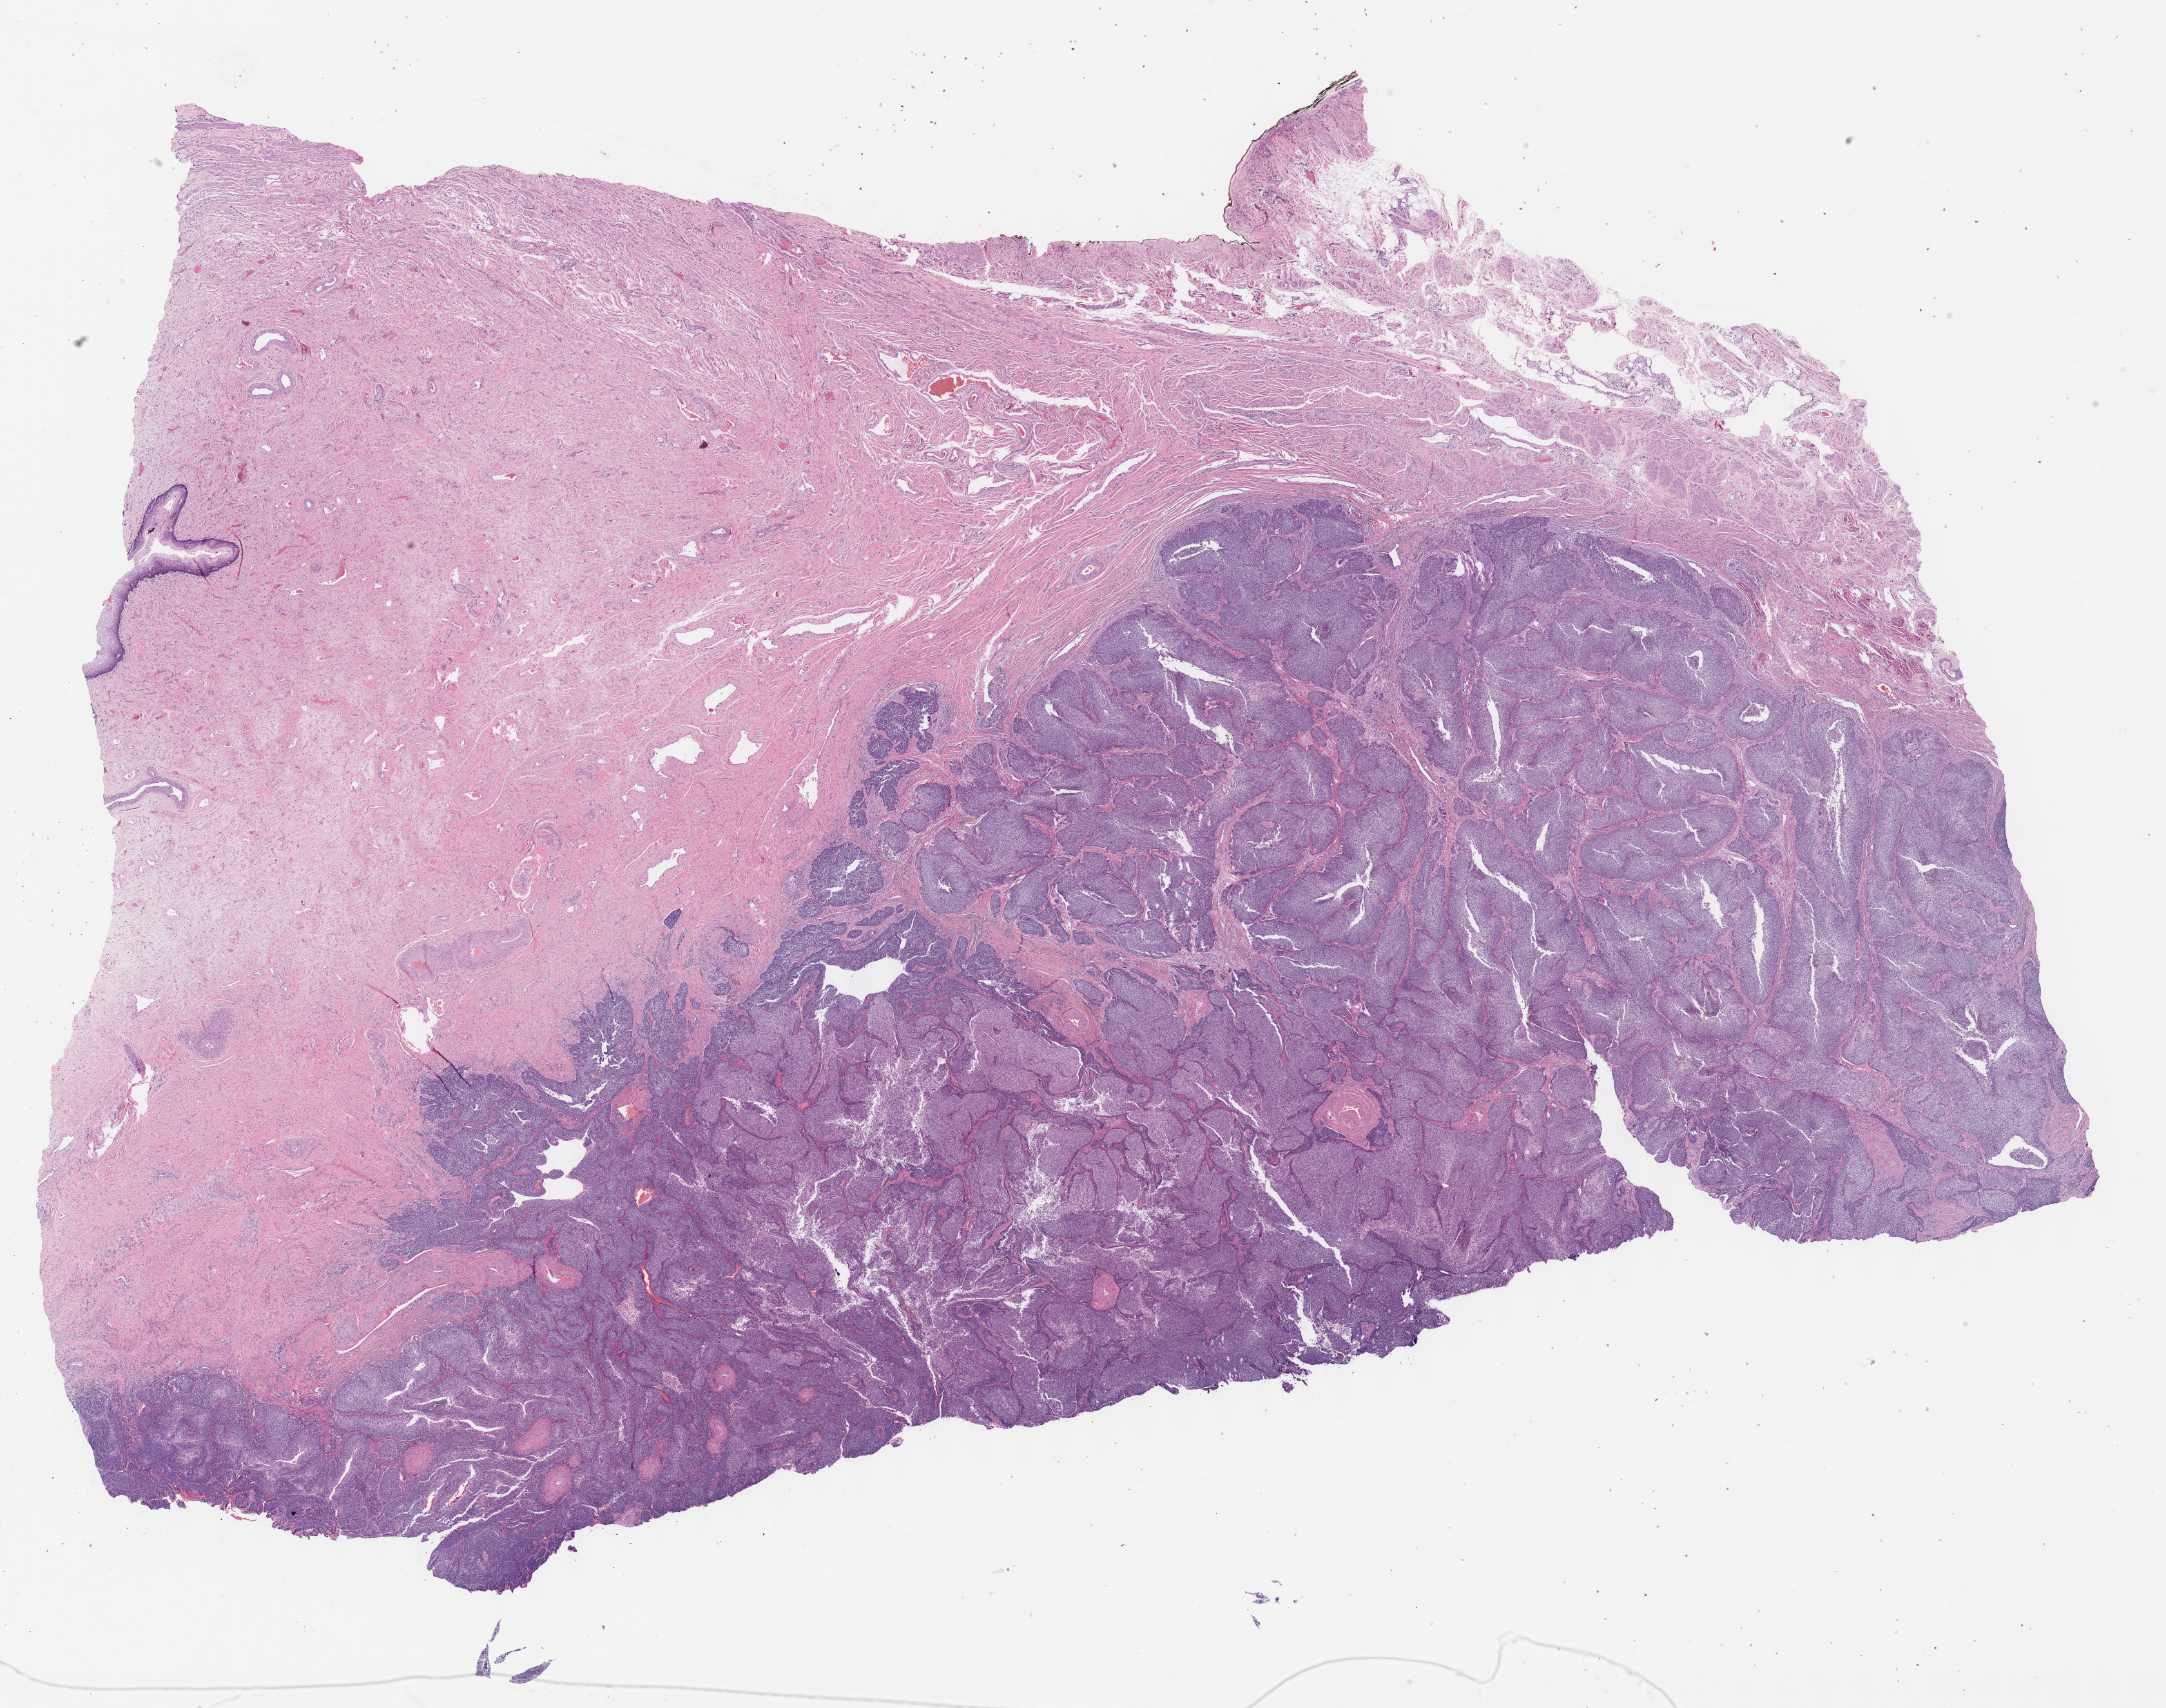
H&E-stained whole-slide image — a low-resolution overview of the entire scanned area, about 27.2 x 21.4 mm (acquisition: 40x scan), formalin-fixed paraffin-embedded (FFPE) diagnostic section, sample: primary tumour, cervix. Female patient; age at initial diagnosis 46 years. Histologic grade: G2 (moderately differentiated).
FIGO stage: IB1. Lymph nodes positive (case pathology): 0 of 15 examined. Pathologic diagnosis: Squamous cell carcinoma, large cell, nonkeratinizing, NOS (cervix uteri).